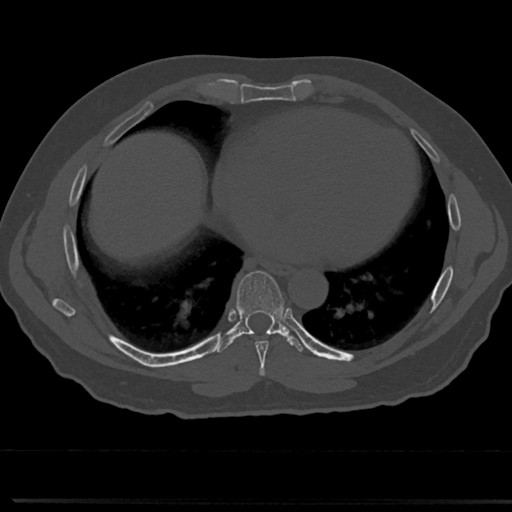
CT including the spine, one axial slice. Slice 372 of 817 in the series (ordered by position). Reconstruction kernel Br40s/3. 120 kVp. Bone window (W 1800 / L 400 HU). 512 × 512 image matrix. Male patient, age 61 years. From the clinical record (not read from this slice): primary cancer: prostate.
Annotated regions visible in this slice (semi-automatic segmentation, software-assisted and operator-edited):
- T7 vertebra: bounding box <235,271,287,358> (left, top, right, bottom; pixels)
- T8 vertebra: <237,325,282,334>